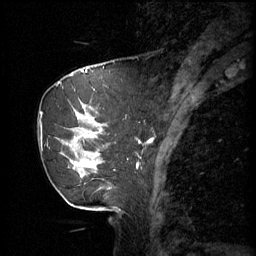
Breast MRI (dynamic contrast-enhanced), one sagittal slice. Position 17 of 60 along the scan axis. 3 images stored at this slice position (order not interpretable as contrast timing). 1.5 T. TE 4.2 ms, TR 11 ms. 2 mm slice thickness. 256 × 256 image matrix. Patient: female, 69 years.
Outlined on this slice (semi-automatically segmented with operator editing):
- analysis volume of interest (the breast-tissue region the enhancement analysis was run in; not a lesion): box from (x=41, y=88) to (x=116, y=189) px
- tumour enhancement mask (voxels above the 70 % enhancement threshold inside the analysis volume of interest): (x=71, y=104)–(x=102, y=165)